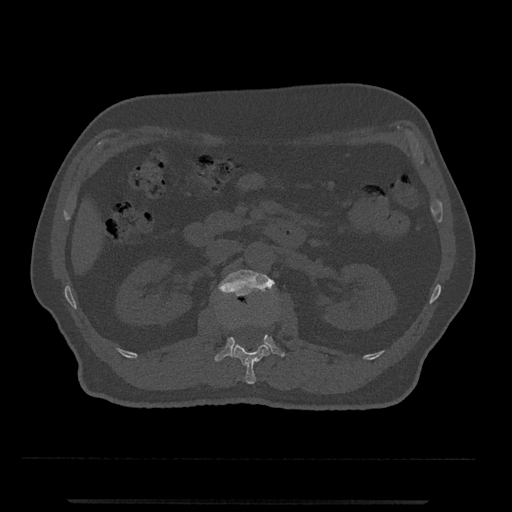
CT including the spine, one axial slice. Position 302 of 797 along the scan axis. Reconstruction kernel Br40s/3. 120 kVp. Bone window (W 1800 / L 400 HU). 512 × 512 image matrix, field of view 419 × 419 mm. Patient: male, 63 years. From the clinical record (not read from this slice): primary cancer: prostate.
Annotated regions visible in this slice (semi-automatically segmented with operator editing):
- L1 vertebra: bounding box (x1, y1, x2, y2) in pixels: (232, 322, 270, 384)
- L2 vertebra: (214, 269, 285, 362)